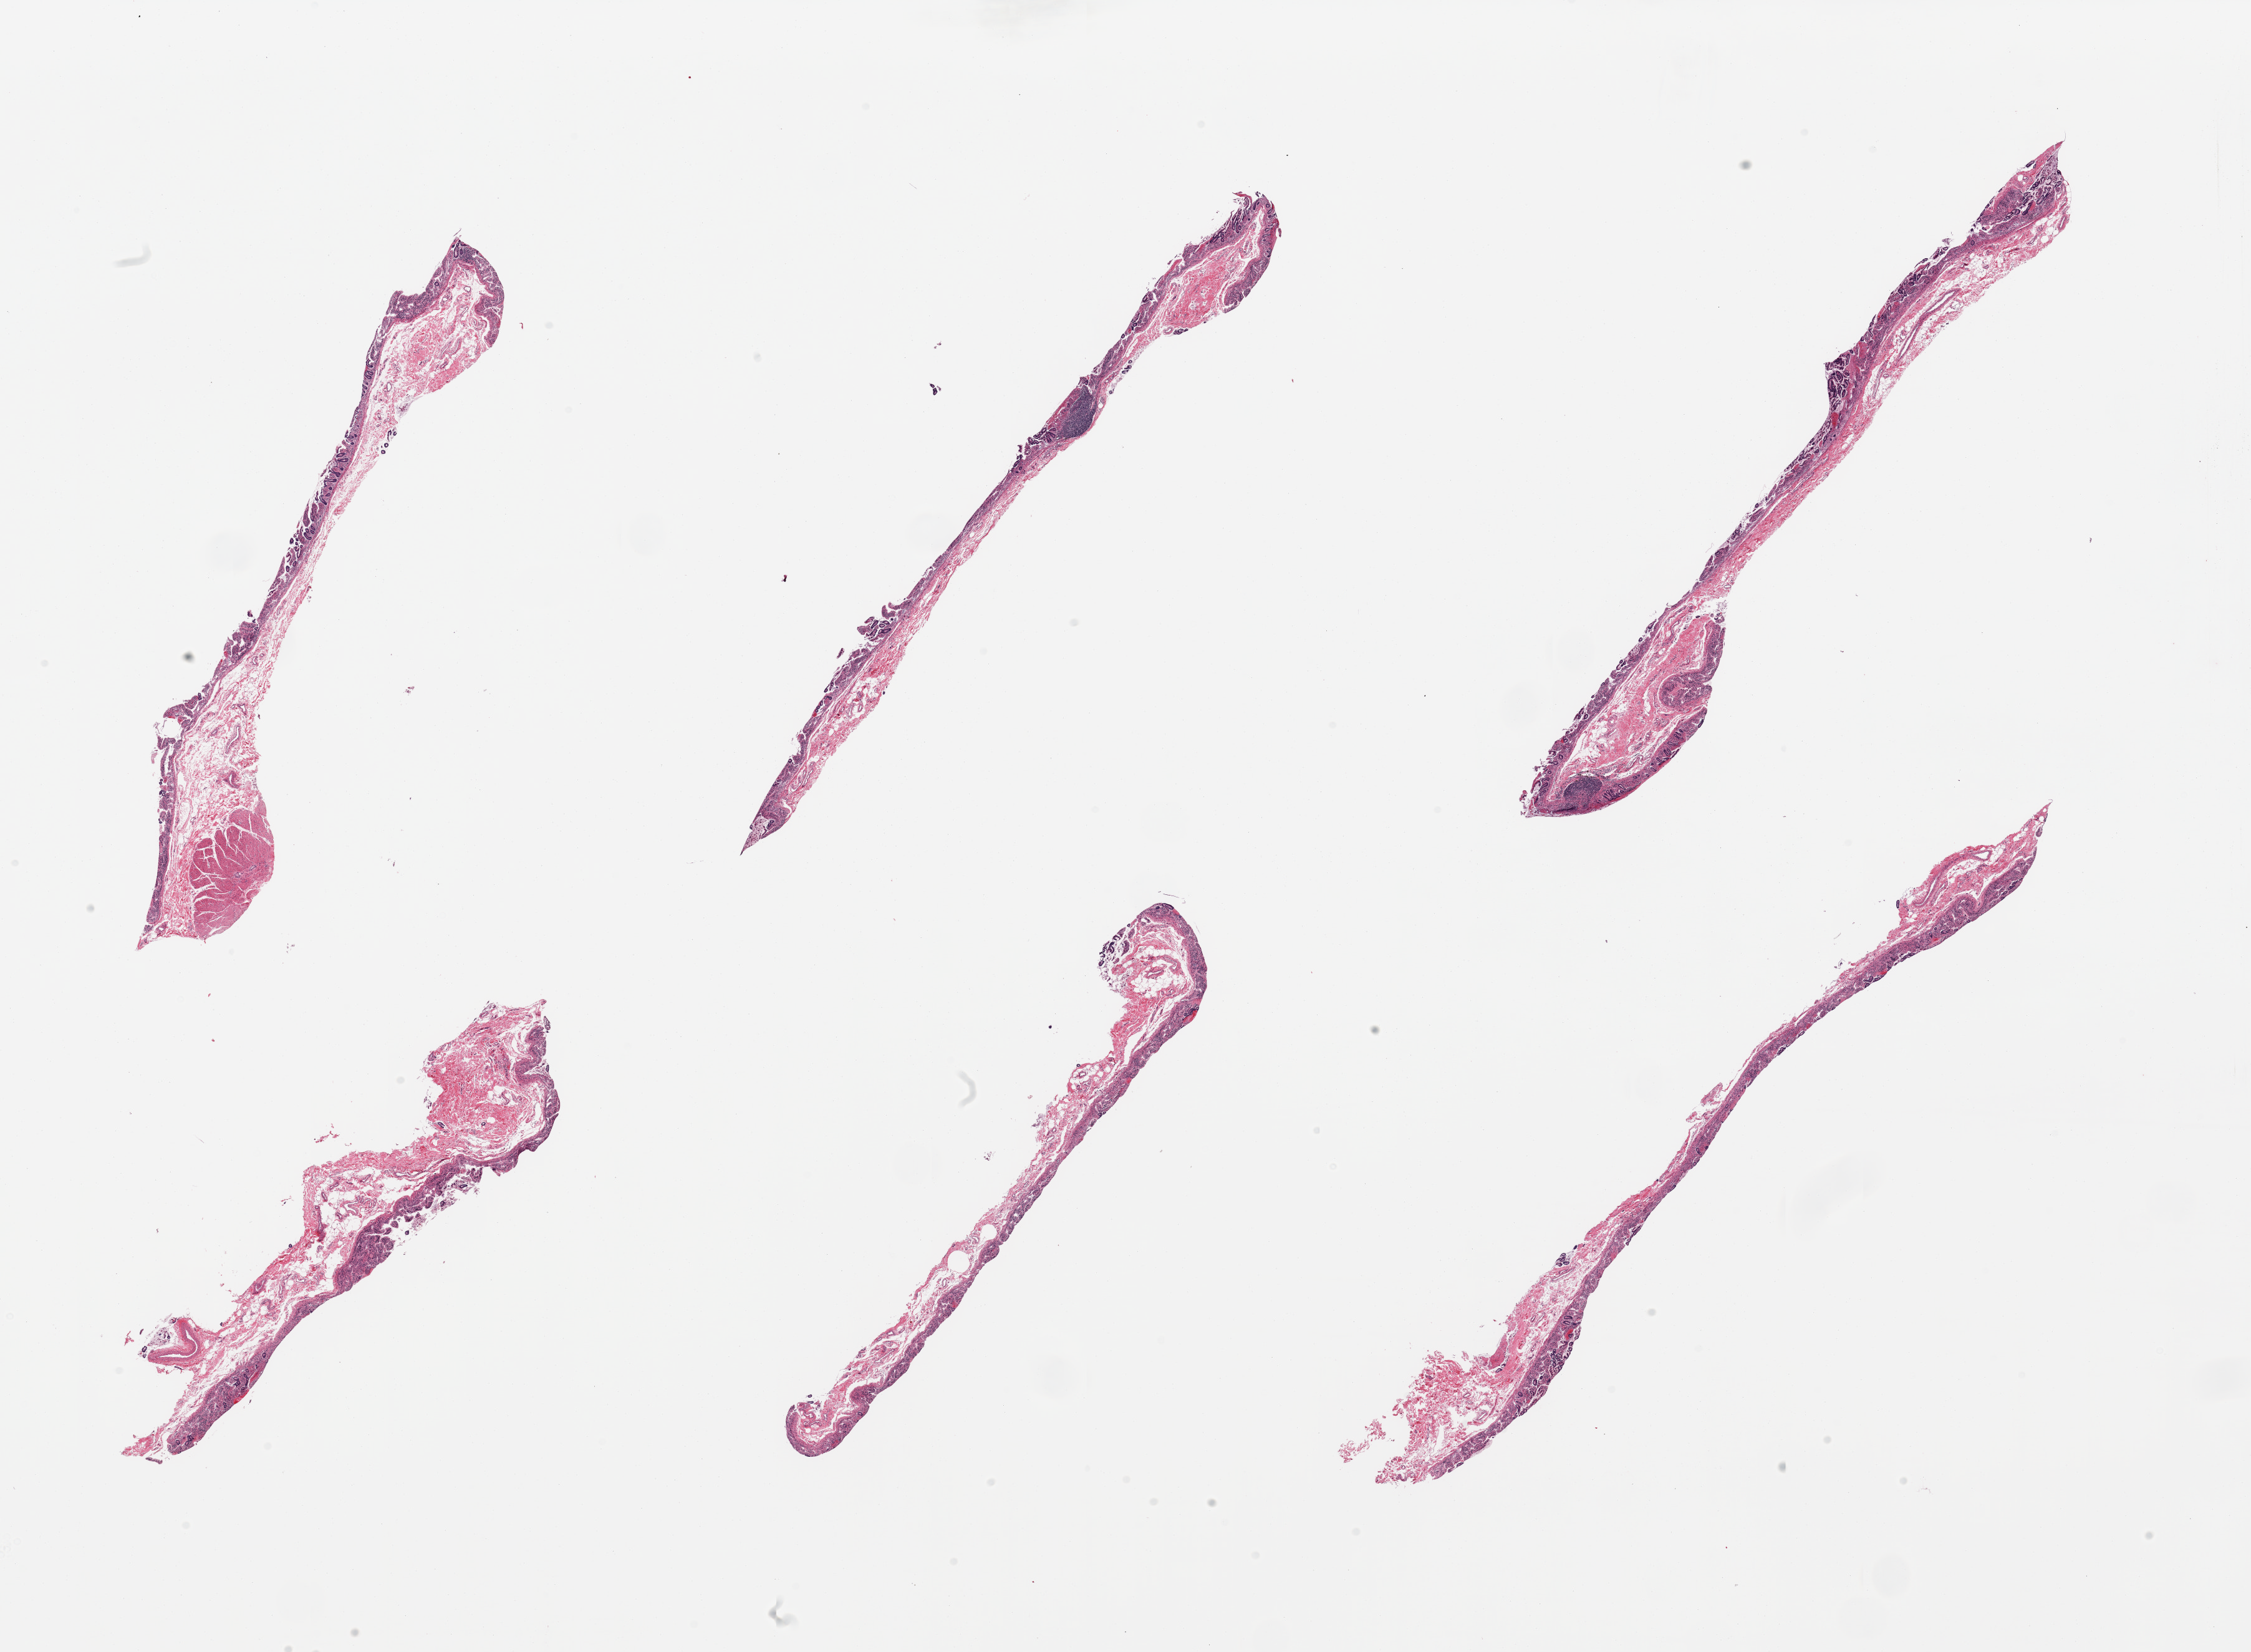
Digitized haematoxylin and eosin-stained section — whole scanned area (about 28.5 x 20.9 mm) shown as a low-resolution overview; PAXgene-fixed, paraffin-embedded tissue; target tissue: ileum; donor tissue sample. Donor: male.
Review note (as recorded): 6 pieces; no significant lymphoid component.